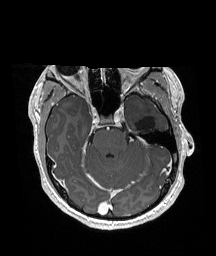
Brain MRI from a brain-tumour surgery series, one axial slice; slice 120 of 192 in the series (ordered by position); T1-weighted post-contrast; 1 mm slice thickness; 216 × 256 image matrix, field of view 211 × 250 mm. From the clinical record (not read from this slice): histopathology: Glioneuronal tumor; WHO grade: 2; tumour location: Left Superior Temporal Gyrus.
Annotated regions visible in this slice (outlined manually by an expert reader):
- previous resection cavity: bounding box (x1, y1, x2, y2) in pixels: (136, 116, 156, 134)